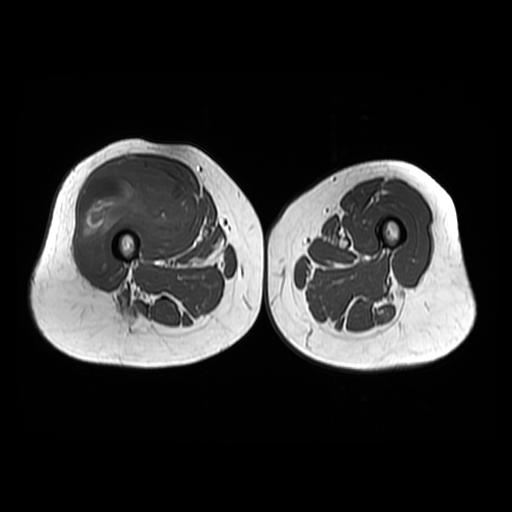
MRI of an extremity soft-tissue mass, one axial slice. Position 26 of 48 along the scan axis. 512 × 512 image matrix, field of view 440 × 440 mm. Female patient. From the clinical record (not read from this slice): histological type: pleiomorphic undifferentiated sarcoma; grade: high; site of the primary tumour: right quadricep.
Outlined on this slice (manually delineated by an expert):
- gross tumour volume including surrounding oedema: bounding box <76,159,197,274> (left, top, right, bottom; pixels)
- gross tumour volume (mass): <76,159,197,274>